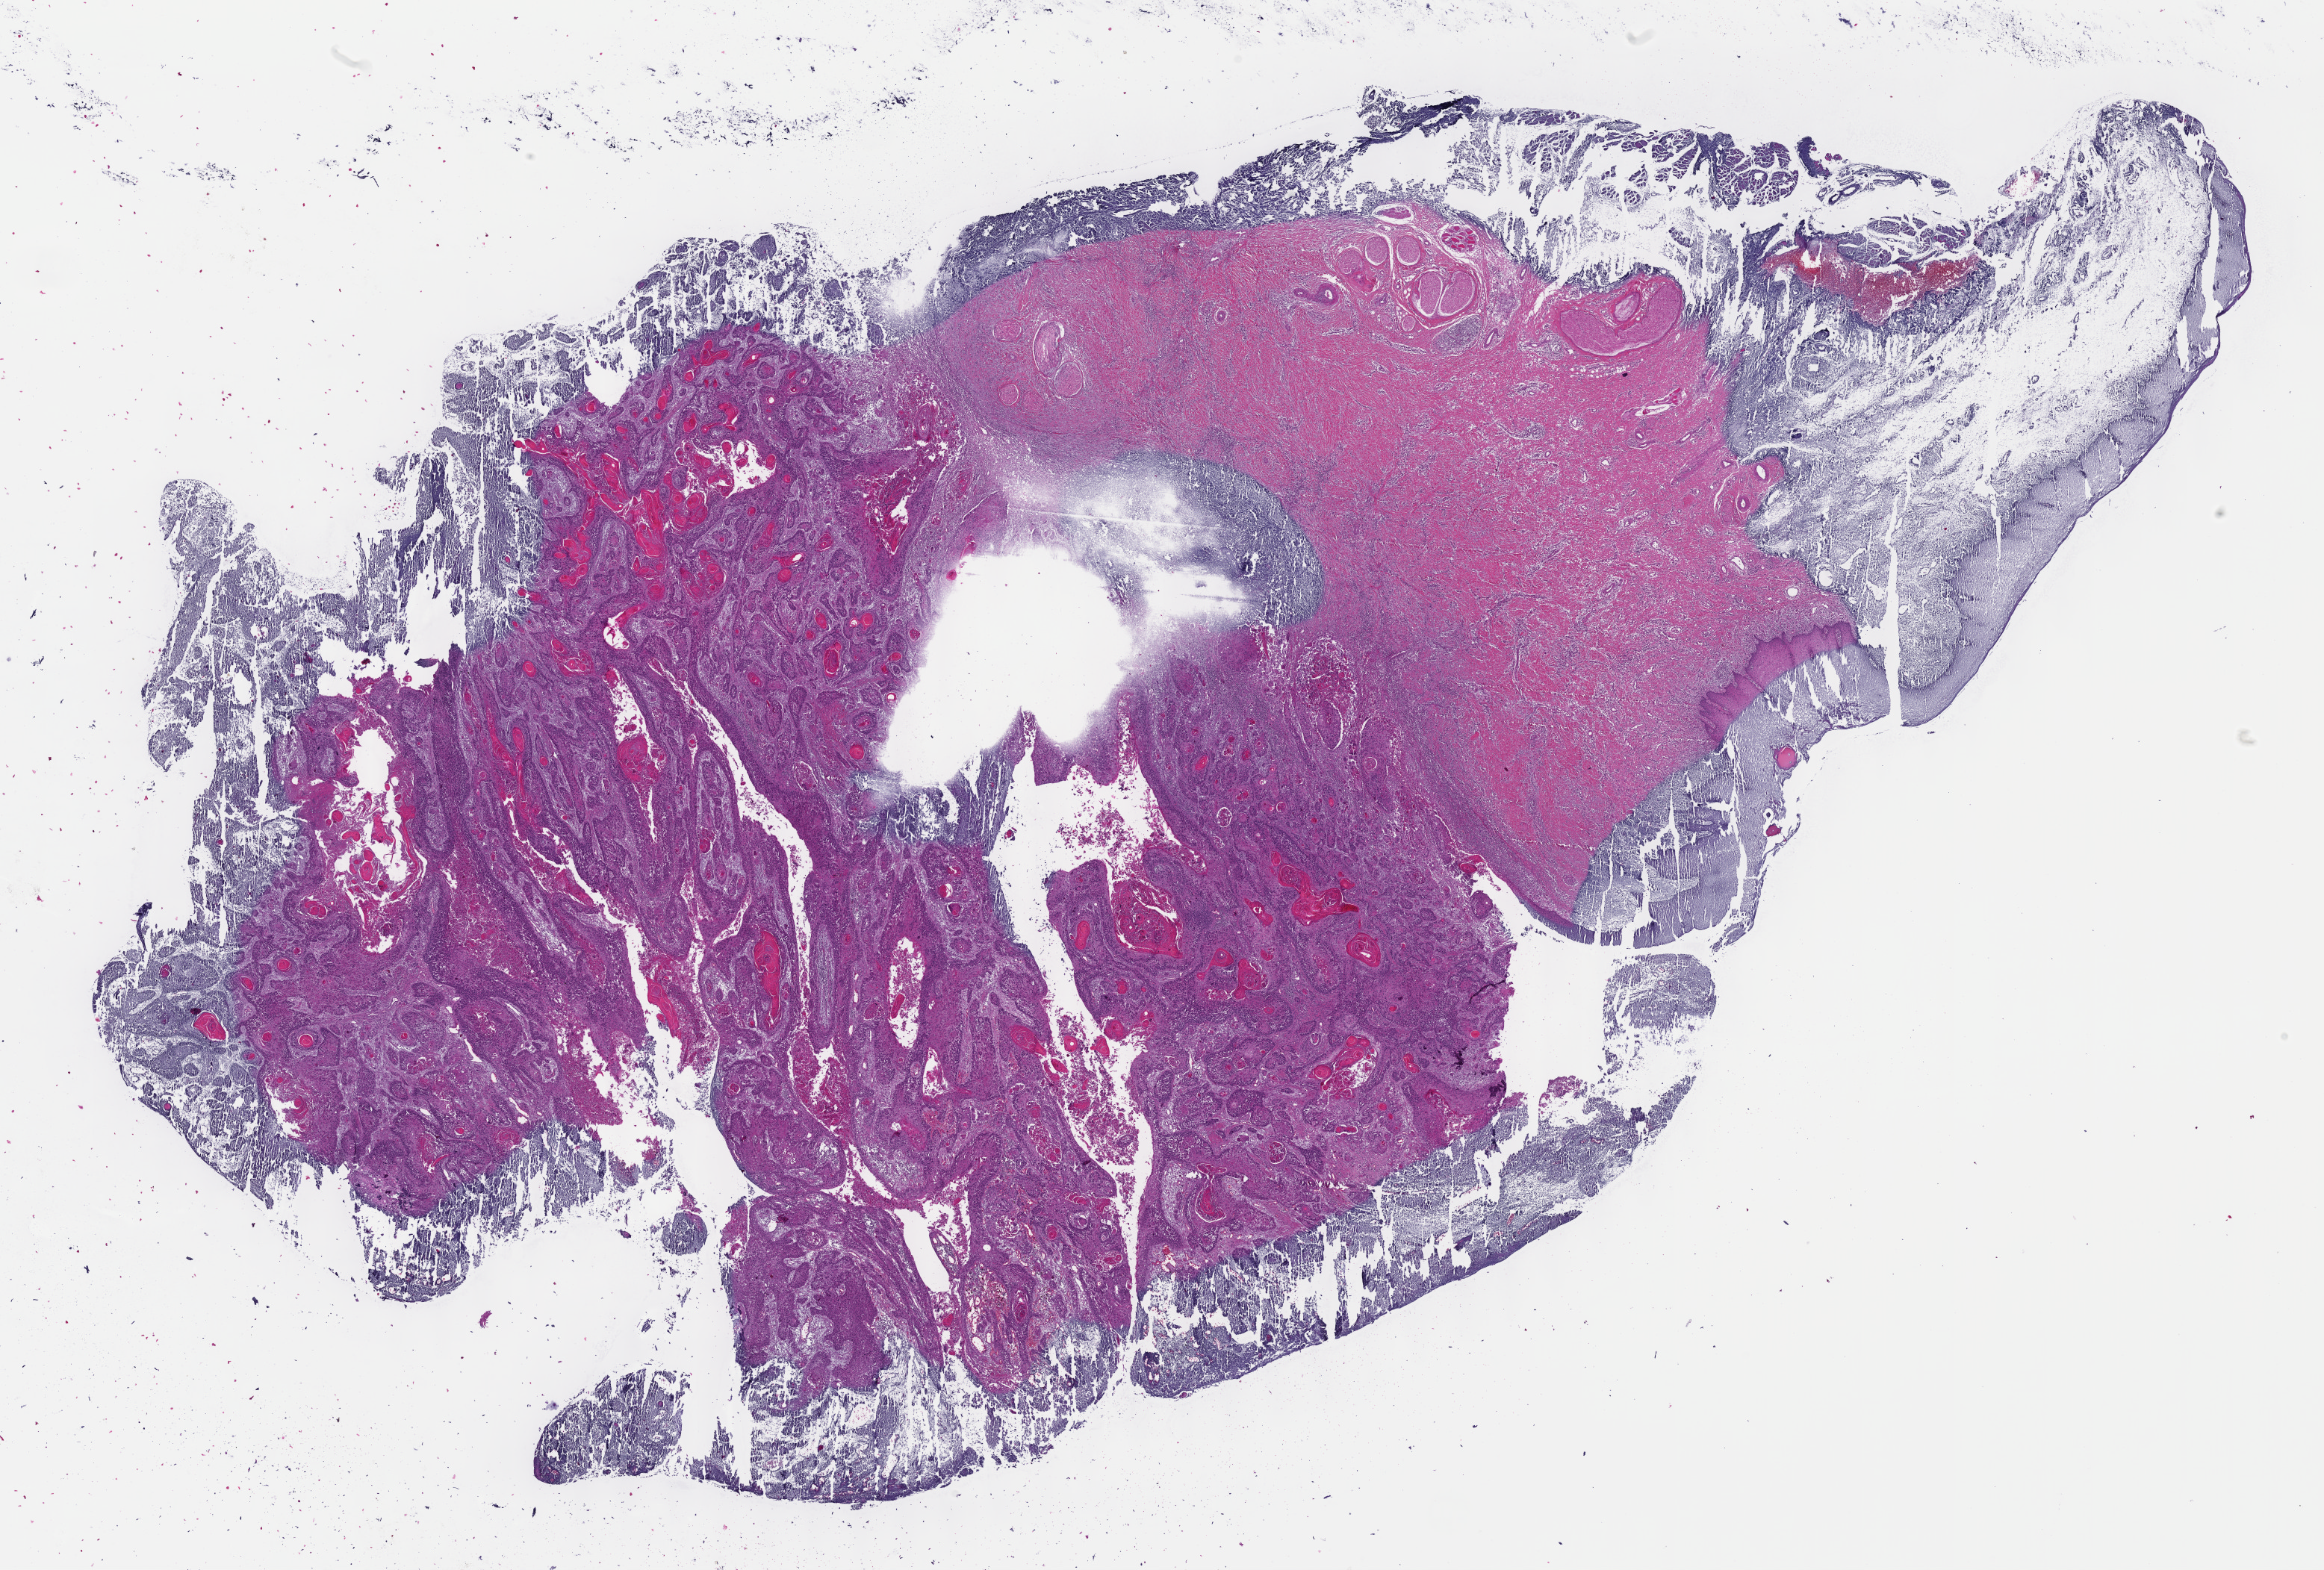
Hematoxylin and eosin (H&E) stained whole-slide image — shown as a low-resolution overview of the whole scanned area (about 25.1 x 17.0 mm); formalin-fixed paraffin-embedded (FFPE) diagnostic section; head and neck, primary tumour sample. Male patient; age at initial diagnosis 53 years. Histologic grade: G2 (moderately differentiated).
* AJCC pathologic stage: III (7th edition)
* histologic diagnosis: Squamous cell carcinoma, NOS (tongue, NOS)
* lymph nodes positive (case pathology): 1 of 32 examined